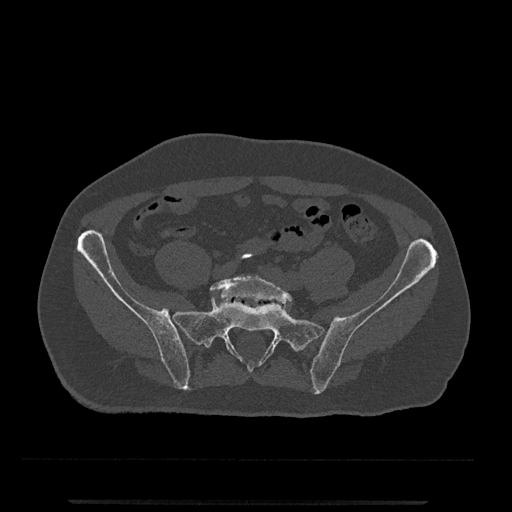
CT including the spine, one axial slice. Position 28 of 797 along the scan axis. 120 kVp. Bone window (W 1800 / L 400 HU). 0.5 mm slice thickness. 512 × 512 image matrix, field of view 419 × 419 mm. Patient: male, 63 years. From the clinical record (not read from this slice): primary cancer: prostate.
Structures marked on this image (semi-automatic segmentation, software-assisted and operator-edited):
- L5 vertebra: bounding box (x1, y1, x2, y2) in pixels: (210, 275, 292, 307)